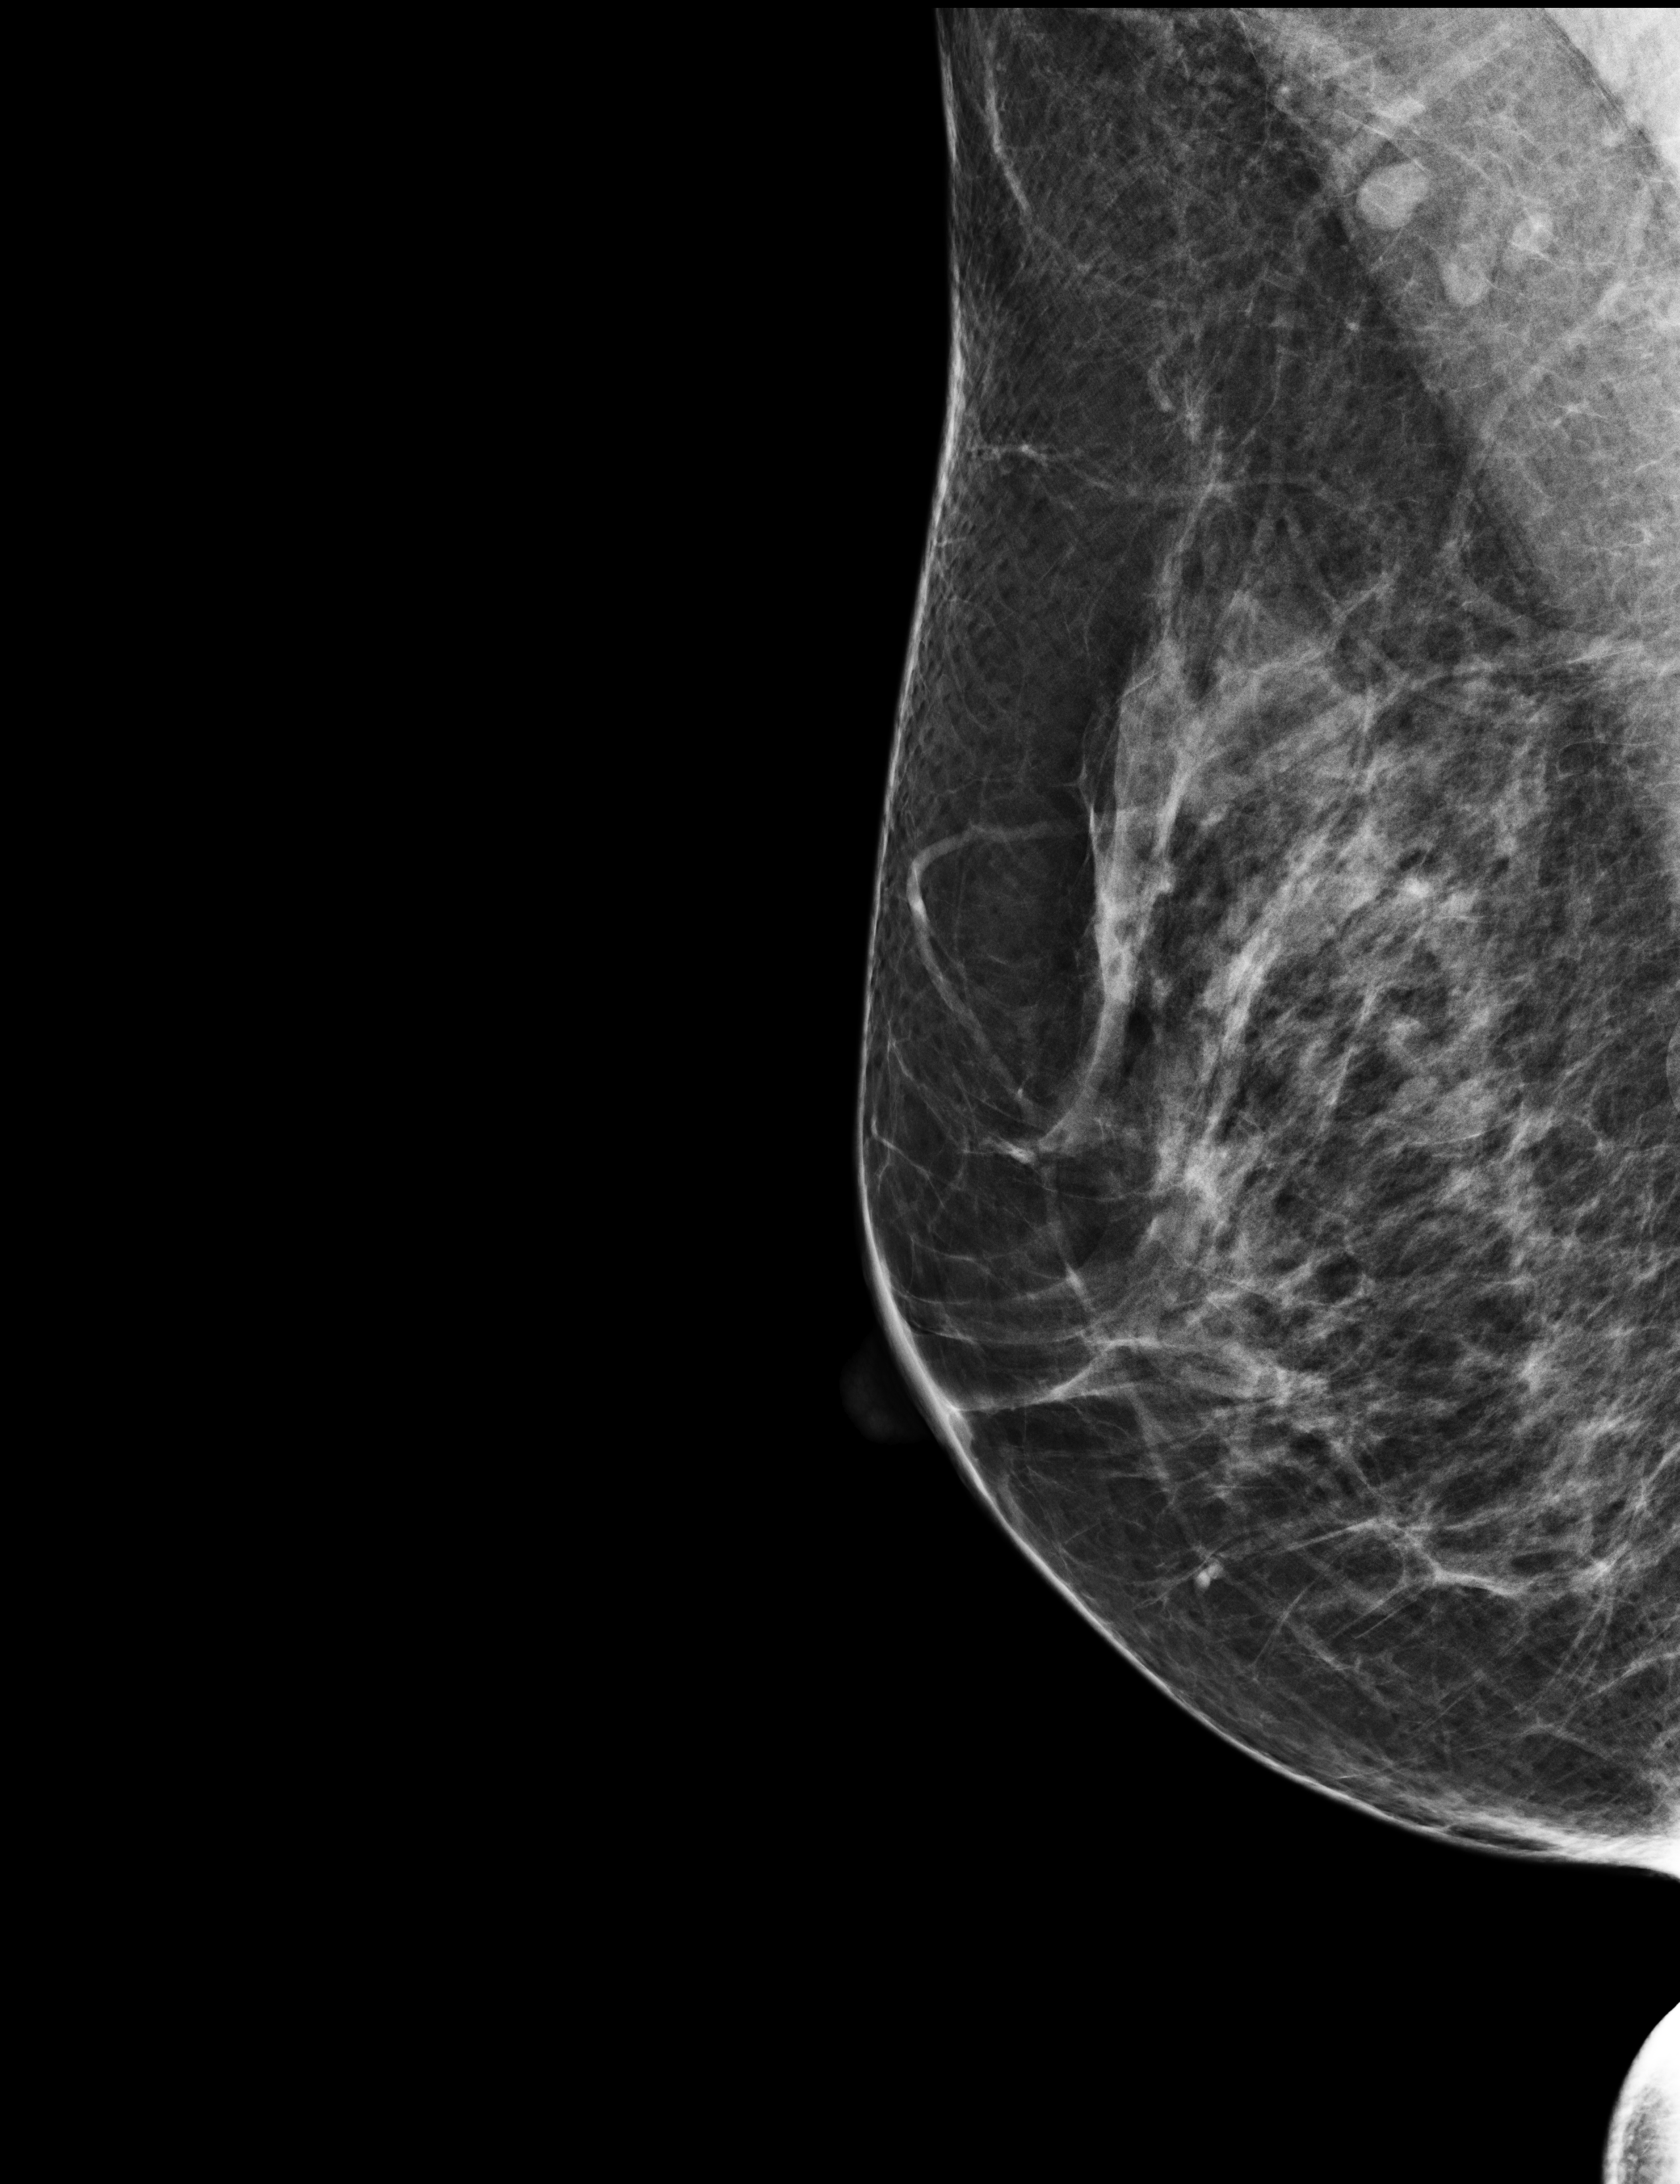
Screening examination; compressed breast thickness 72 mm. Patient: female, 54 years.
Image type: full-field digital mammogram. Breast: right. Projection: medio-lateral oblique projection.